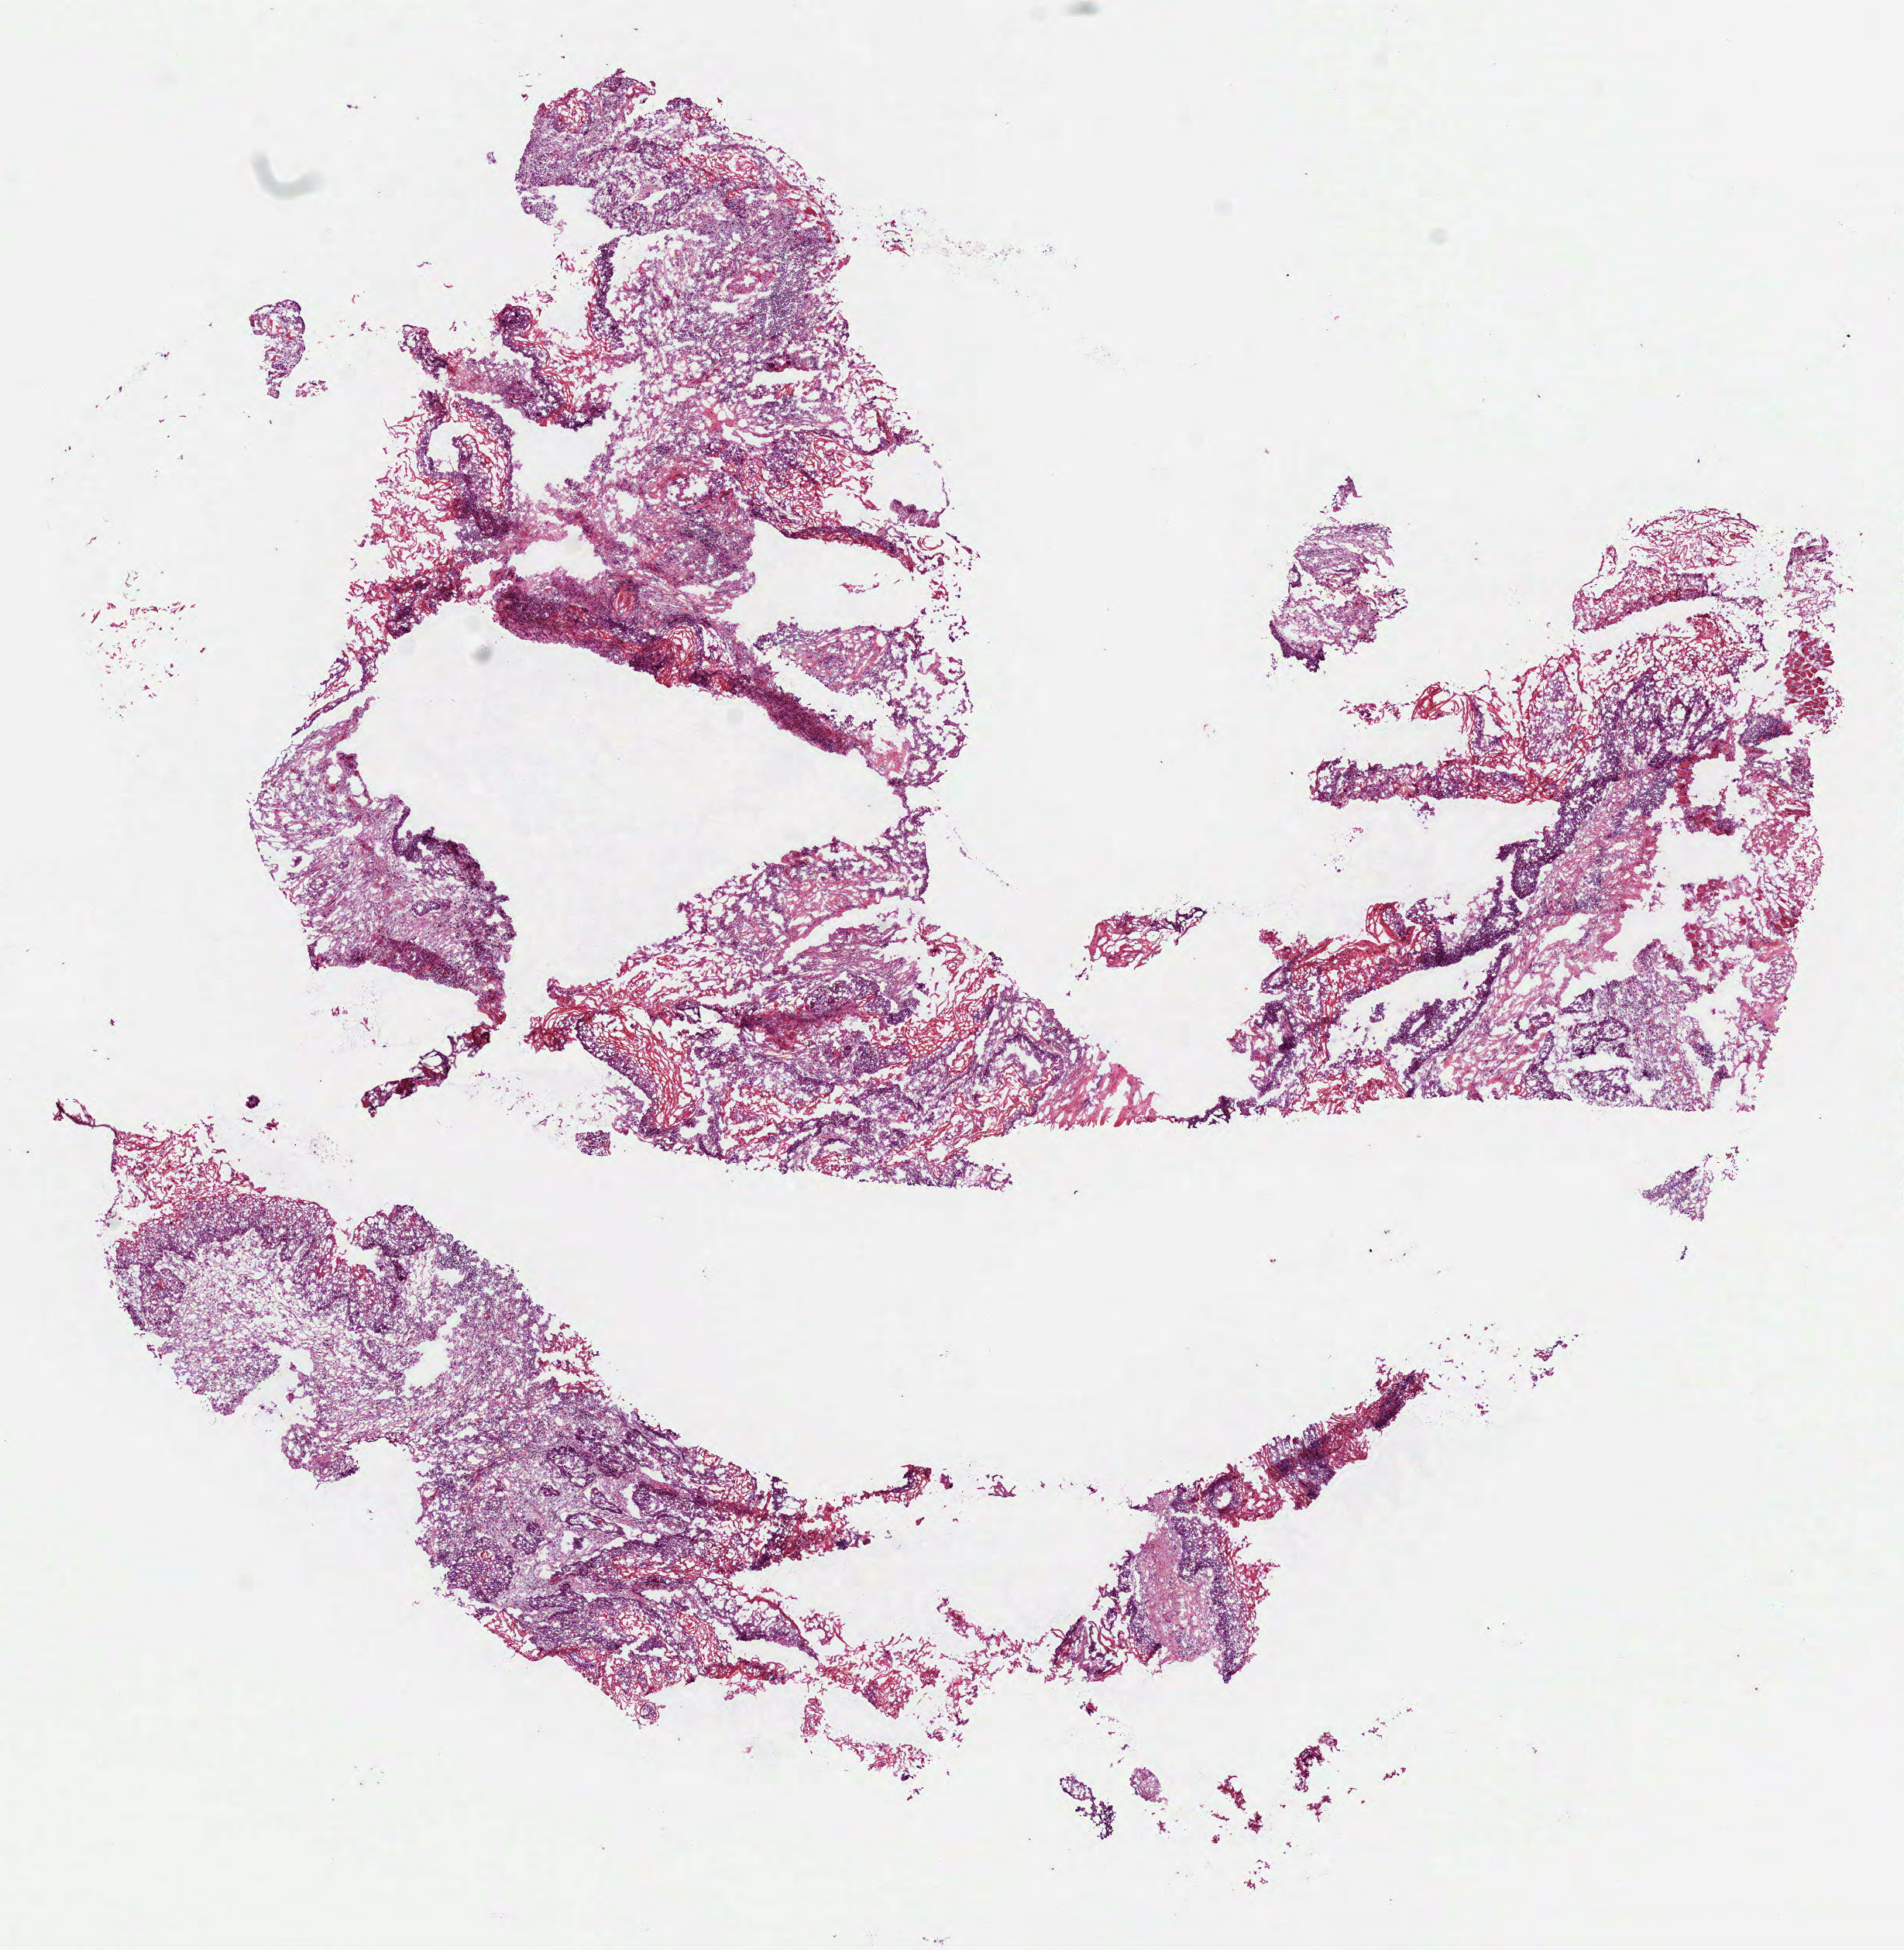
Digitized Hematoxylin and eosin (H&E) stained tissue section (whole slide) — shown as a low-resolution overview of the whole scanned area (about 9.9 x 10.1 mm, from a 40x scan); frozen section from the bottom of the tissue portion; head and neck, primary tumour sample. Male patient; age at initial diagnosis 64 years. Histologic grade: G1 (well differentiated). Slide review estimates, as recorded: tumour cells 80%, tumour nuclei 55%, normal cells 5%, stromal cells 15%, necrosis 0%.
Diagnosis: Squamous cell carcinoma, NOS (overlapping lesion of lip, oral cavity and pharynx). AJCC pathologic stage: II (7th edition). TNM: T2 NX.